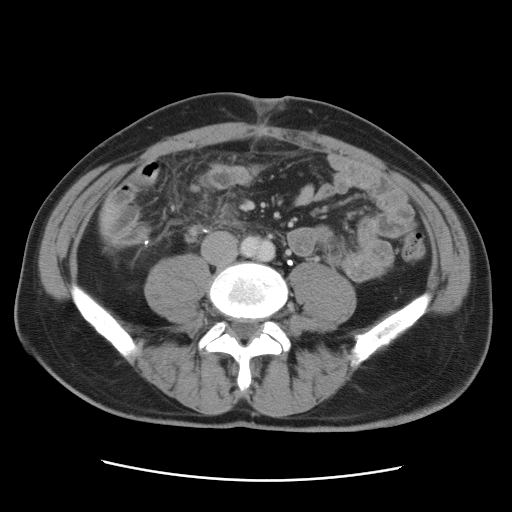
Contrast-enhanced abdominal CT, one axial slice. Position 3 of 89 along the scan axis. 120 kVp. Intravenous contrast given. Soft-tissue window (W 400 / L 40 HU). 5 mm slice thickness. 512 × 512 image matrix, field of view 366 × 366 mm. Male patient, age 59 years. Case-level facts recorded for this patient, not image findings: diagnosis: colorectal cancer liver metastases, imaged before liver resection; multiple liver metastases: yes; largest metastasis: 0.6 cm.
Annotated regions visible in this slice (outlined manually by an expert reader):
- liver: box from (x=100, y=208) to (x=116, y=235) px
- planned liver remnant (the part of the liver to remain after resection): (x=100, y=208)–(x=117, y=234)